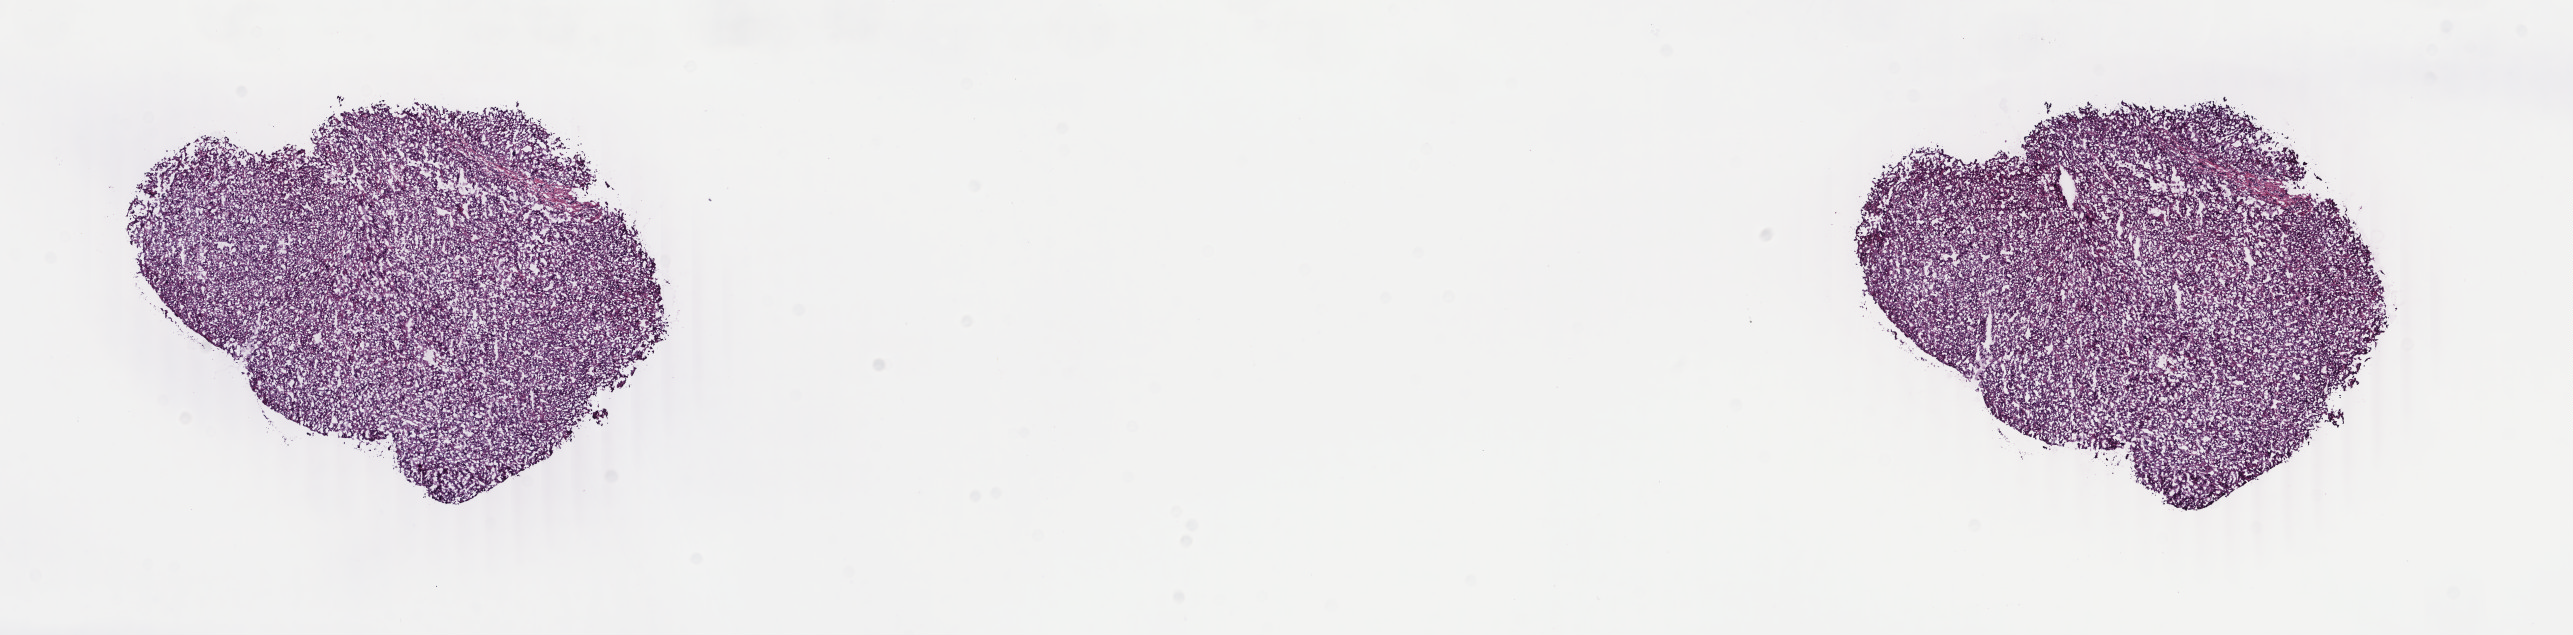
Digitized H&E tissue section (whole slide), a low-resolution overview of the entire scanned area, about 20.5 x 5.1 mm; frozen section; liver, primary tumour sample. Female, age 64 years at initial diagnosis. Pathologist review of this section (percent, as recorded): tumour cells 80%, tumour nuclei 80%.
Diagnosis: Hepatocellular carcinoma, NOS.